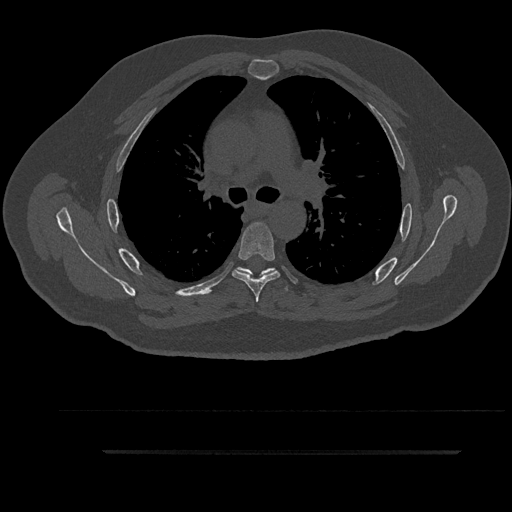
CT including the spine, one axial slice; slice 619 of 797 in the series (ordered by position); reconstruction kernel Br40s/3; 120 kVp; bone window (W 1800 / L 400 HU); 0.5 mm slice thickness; 512 × 512 image matrix, field of view 432 × 432 mm. Patient: male, 63 years. From the clinical record (not read from this slice): primary cancer: renal; vertebrae with lytic lesions (as recorded): T8.
Structures marked on this image (semi-automatic segmentation, software-assisted and operator-edited):
- T5 vertebra: bounding box <232,222,280,302> (left, top, right, bottom; pixels)
- T6 vertebra: <237,267,292,292>